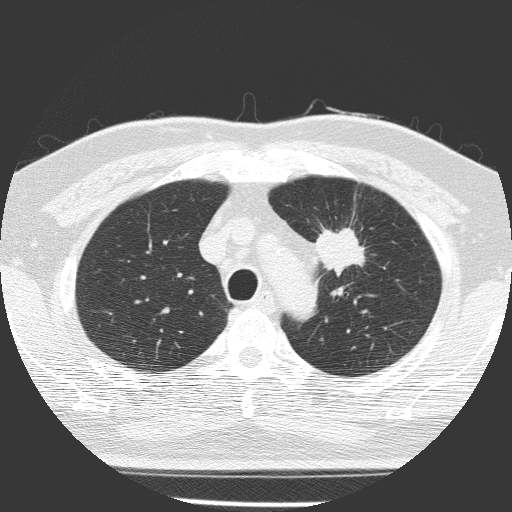
Low-dose screening chest CT, one axial slice; slice 118 of 156 in the series (ordered by position); 120 kVp; lung window (W 1500 / L -600 HU); 2 mm slice thickness; 512 × 512 image matrix, field of view 309 × 309 mm.
Annotated regions visible in this slice (outlined manually by an expert reader):
- lesion 1 (tumor, upper lobe of left lung): bounding box (x1, y1, x2, y2) in pixels: (316, 228, 365, 275)